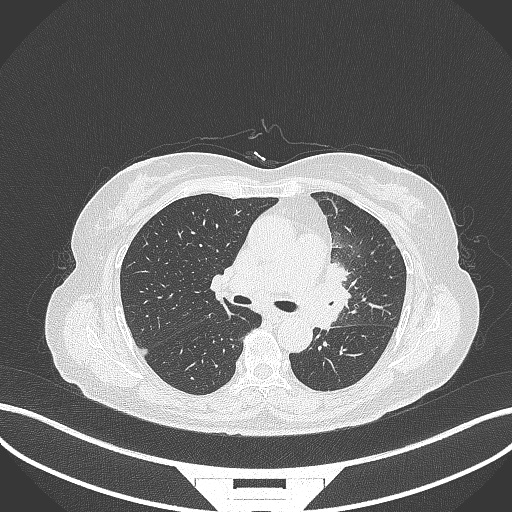
Chest CT, one axial slice; reconstruction kernel B70f; 120 kVp; lung window (W 1500 / L -600 HU); 1 mm slice thickness; 512 × 512 image matrix, field of view 400 × 400 mm. Patient: female, 64 years. Case-level facts recorded for this patient, not image findings: clinical TNM (as recorded): T2a N2 M0.
Annotated regions visible in this slice (bounding box drawn by a radiologist):
- lung tumour (recorded histology: adenocarcinoma): bounding box <321,256,356,331> (left, top, right, bottom; pixels)